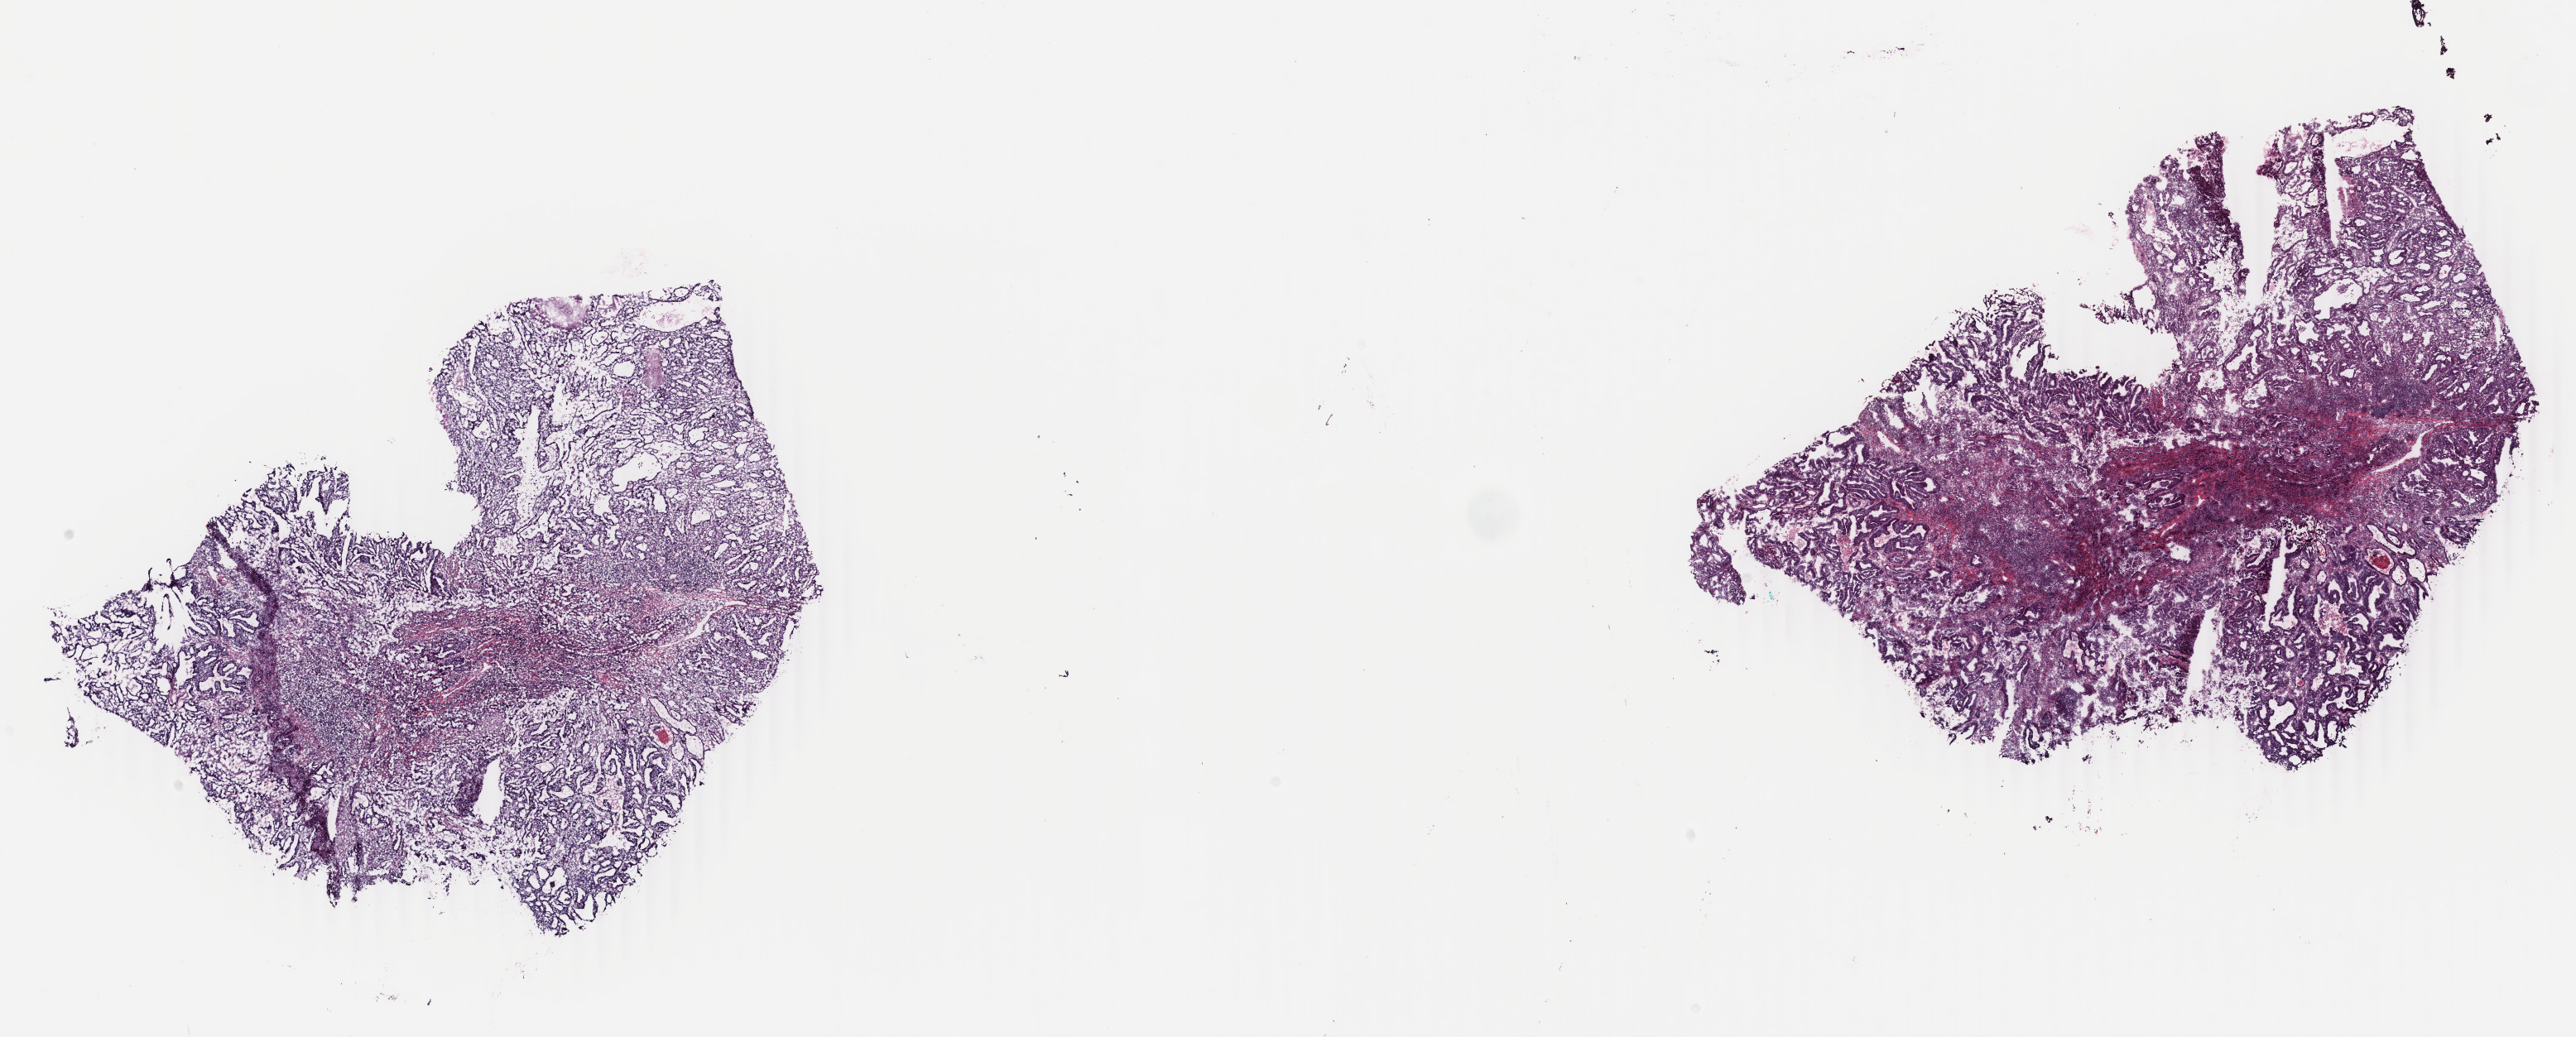
Whole-slide histology image, H&E-stained — a low-resolution overview of the entire scanned area, about 24.7 x 10.0 mm (slide scanned at 40x). Frozen section from the bottom of the tissue portion. Uterus, primary tumour sample. Patient: female, age at initial diagnosis 64 years. Histologic grade: G1 (well differentiated). Pathologist review of this section (percent, as recorded): tumour cells 90%, tumour nuclei 70%, normal cells 0%, stromal cells 10%, necrosis 0%. Inflammatory infiltration, as recorded: lymphocyte infiltration 0%, monocyte infiltration 0%, neutrophil infiltration 0%.
* pathologic diagnosis: Endometrioid adenocarcinoma, NOS (endometrium)
* FIGO stage: IB